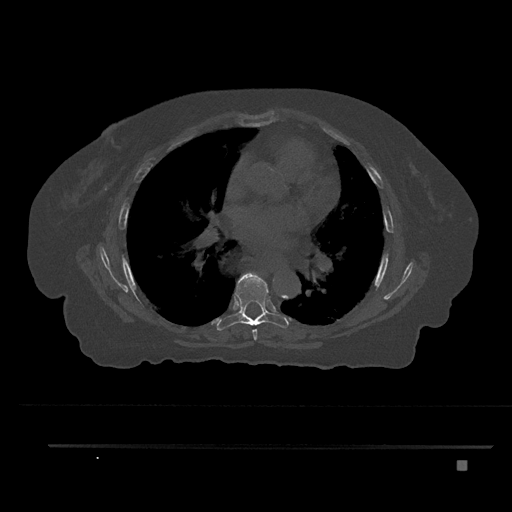
CT including the spine, one axial slice; reconstruction kernel Br40s/3; bone window (W 1800 / L 400 HU); 512 × 512 image matrix, field of view 437 × 437 mm. Female patient, age 76 years. Case-level facts recorded for this patient, not image findings: primary cancer: lung; vertebrae with lytic lesions (as recorded): T11, L3.
Outlined on this slice (semi-automatic segmentation, software-assisted and operator-edited):
- T6 vertebra: bounding box <252,273,263,340> (left, top, right, bottom; pixels)
- T7 vertebra: <216,272,289,331>